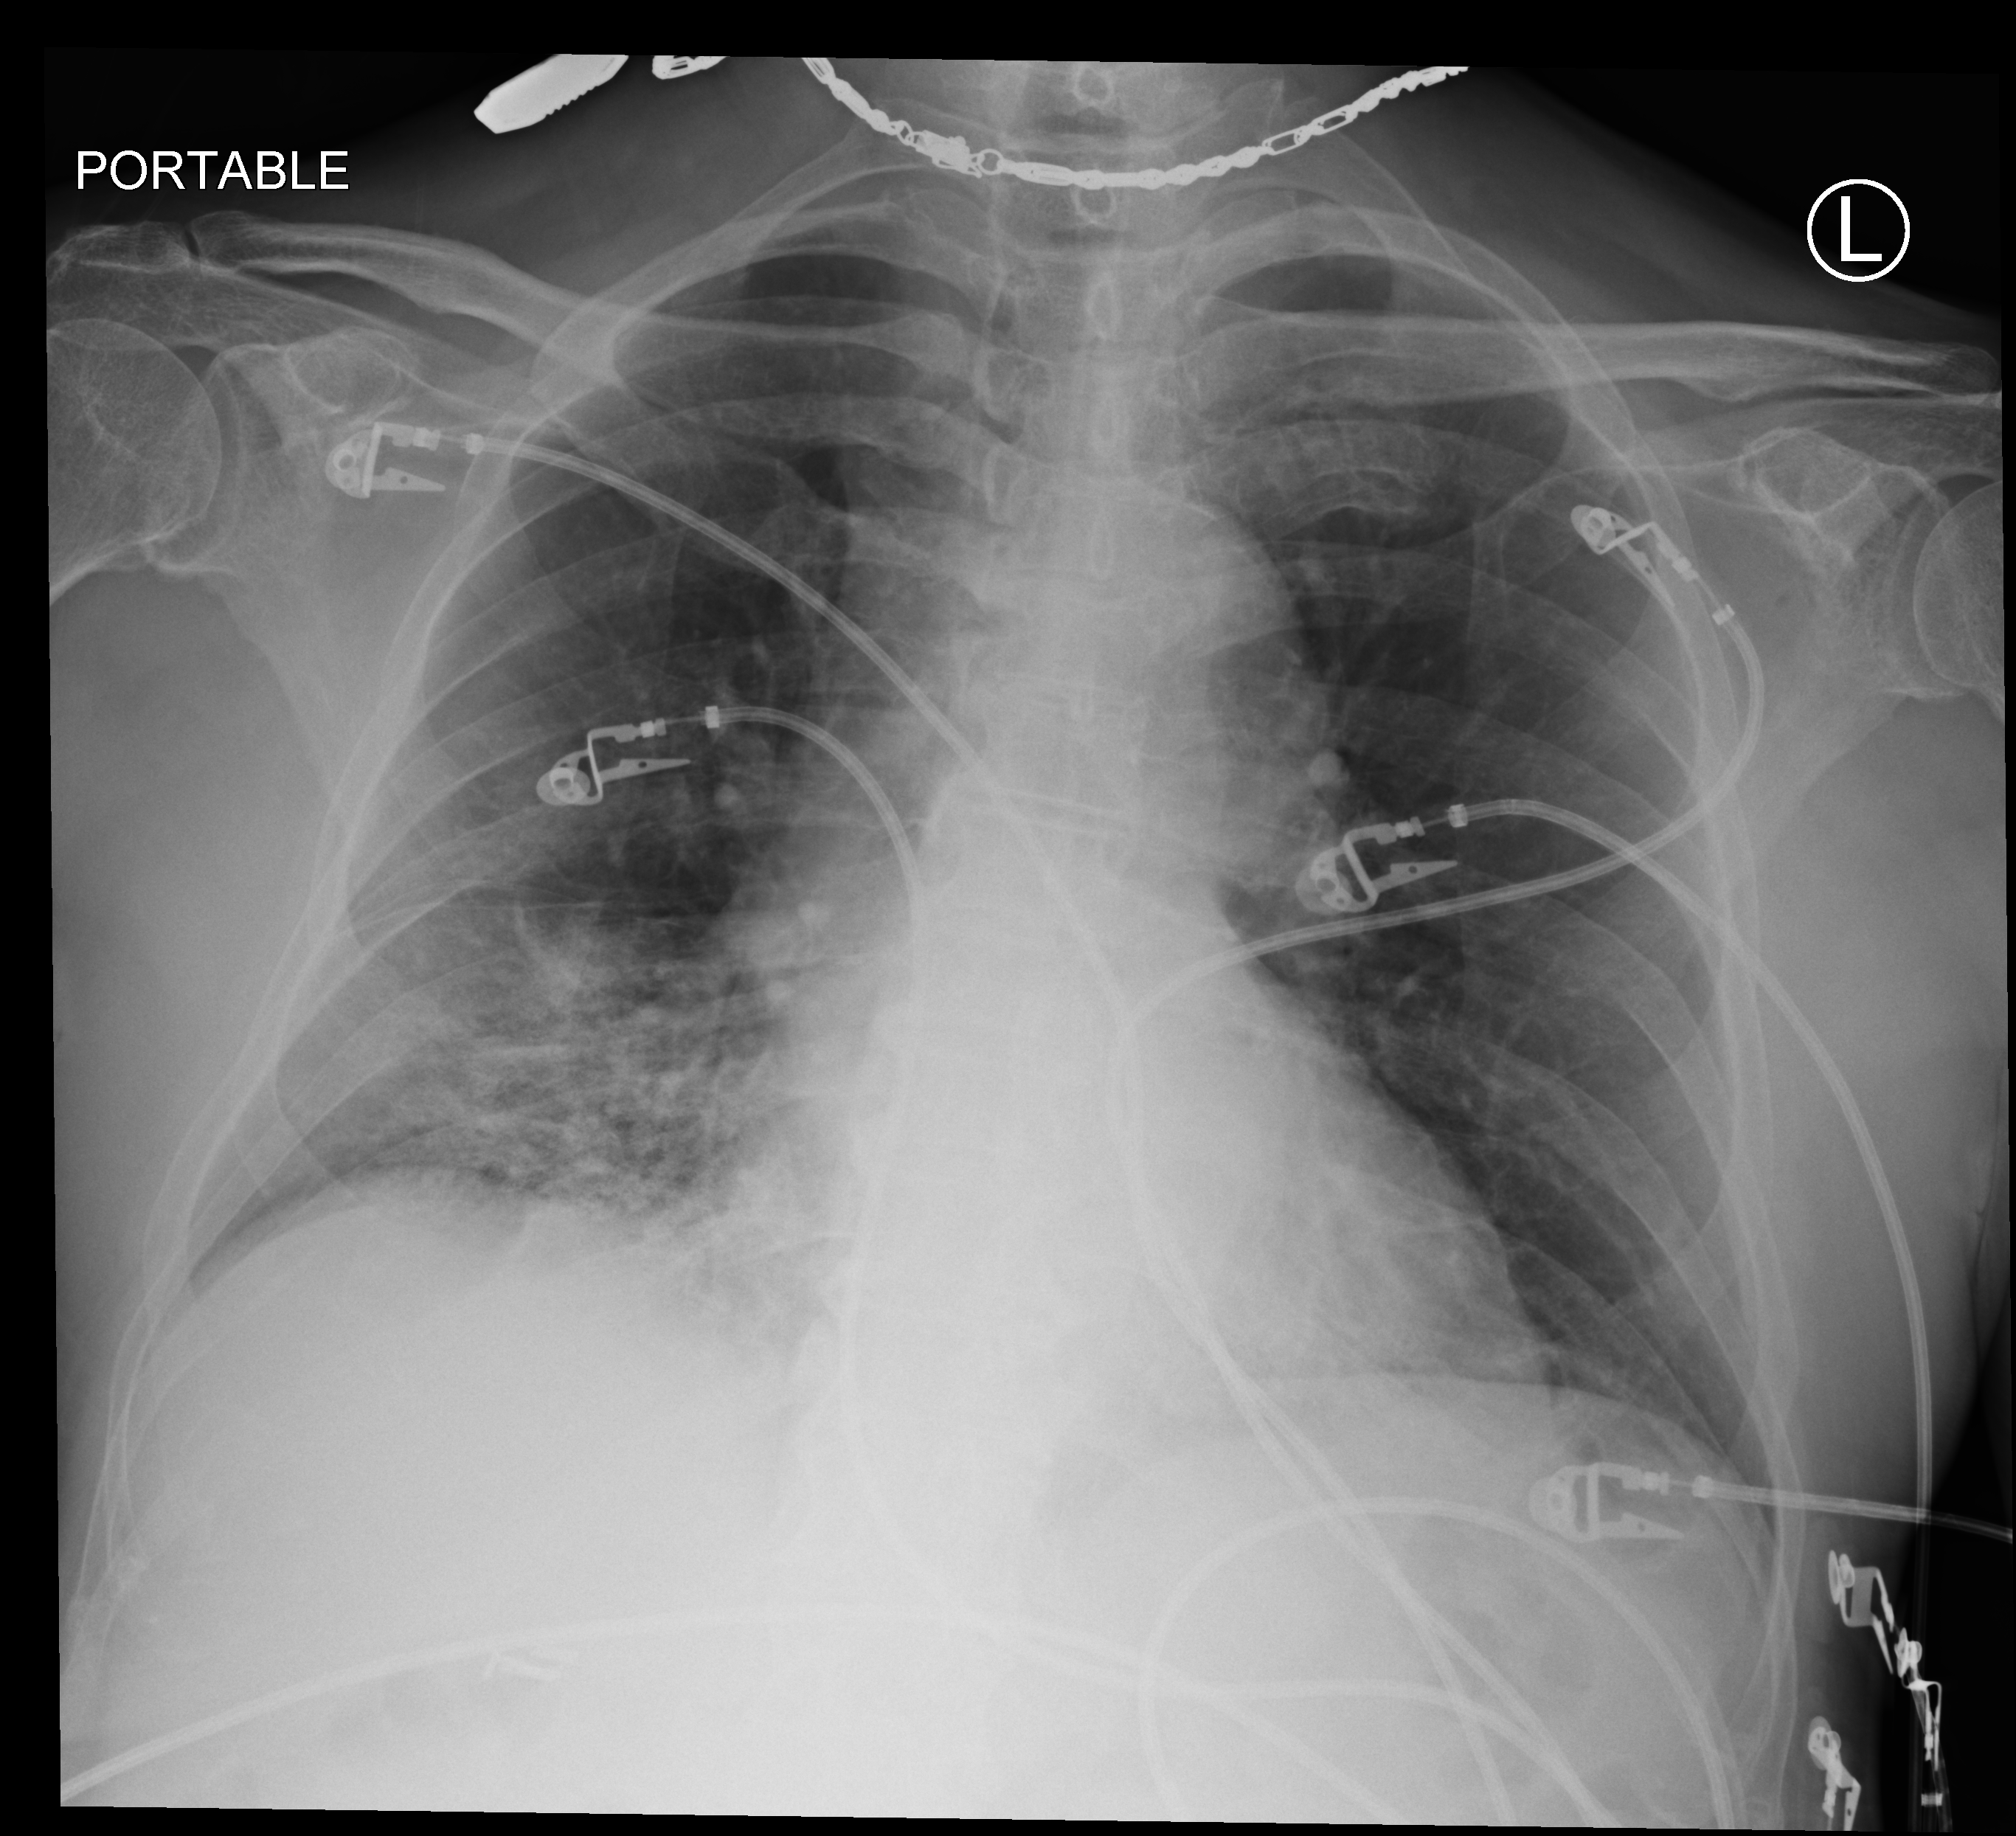
Chest X-ray (portable), anteroposterior (AP) projection. Patient hospitalised with COVID-19; male, aged 75–90 years.
From the hospital-stay record, not from the radiograph (when in the stay this image was taken is not recorded):
- COPD (admission record): no